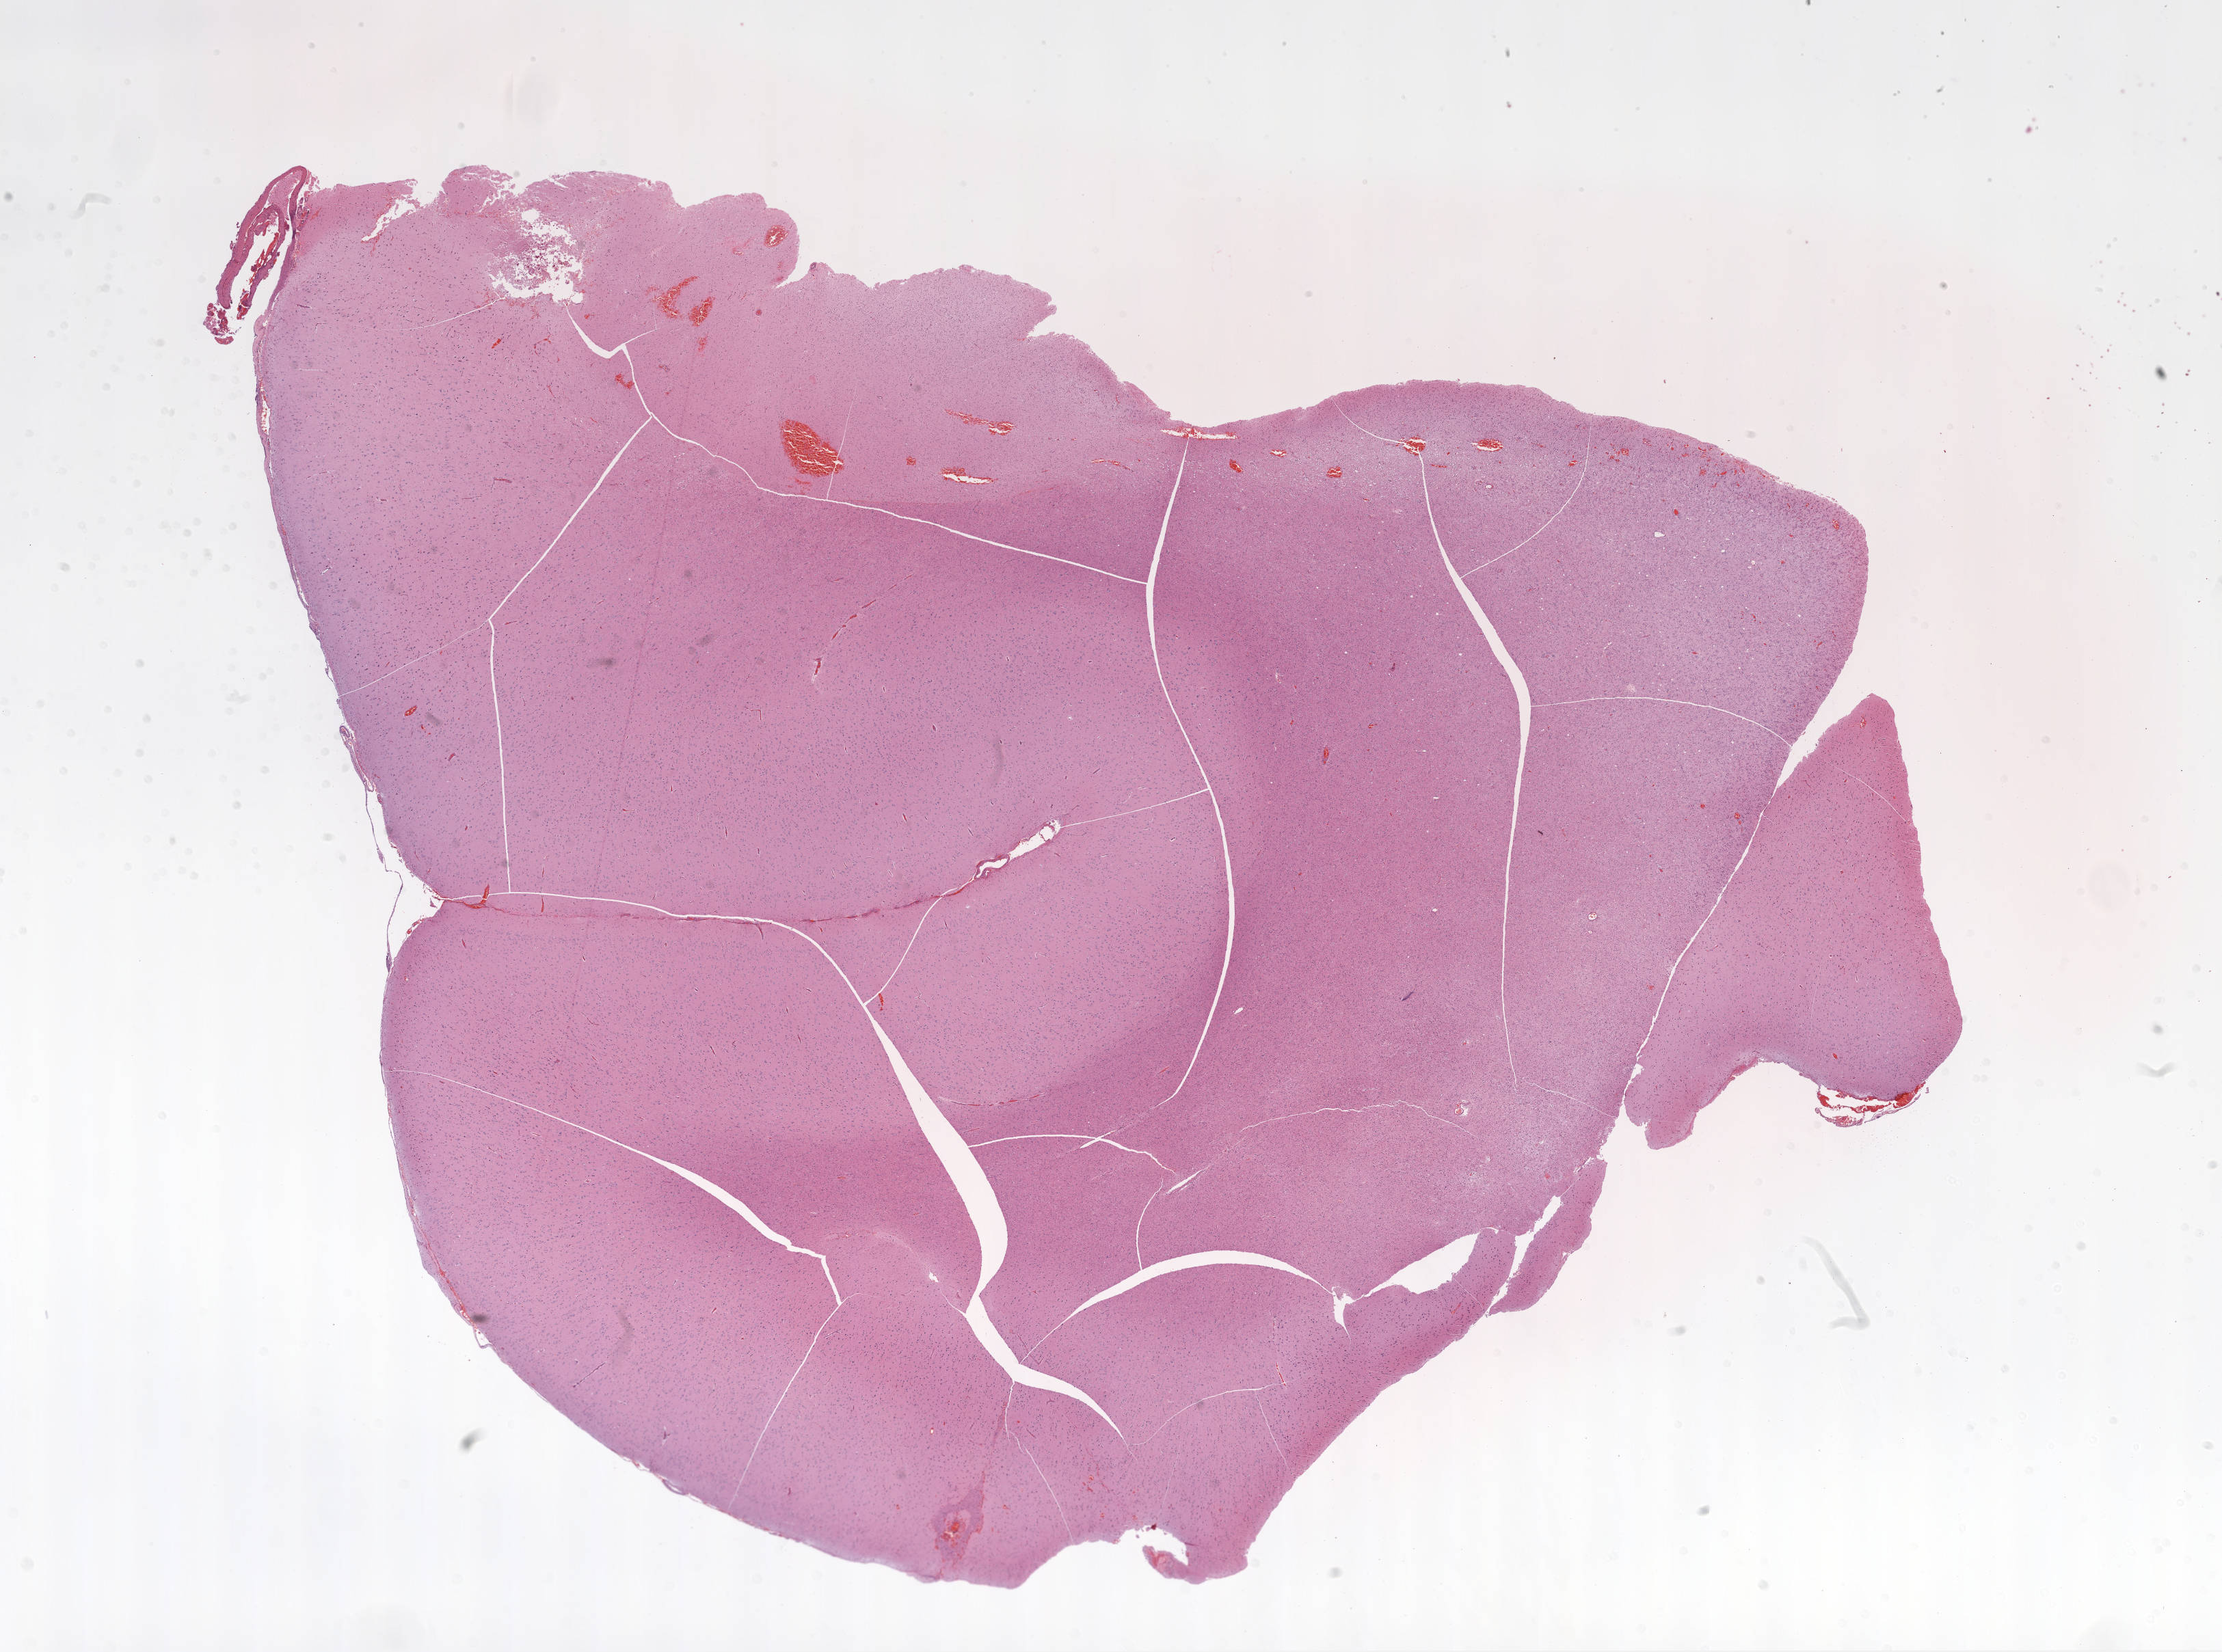
H&E whole-slide image, low-resolution overview of the scanned area, about 26.1 x 19.4 mm (slide scanned at 20x); FFPE section; brain, primary tumour sample. Male, age 71 years at initial diagnosis.
- histologic diagnosis: Glioblastoma